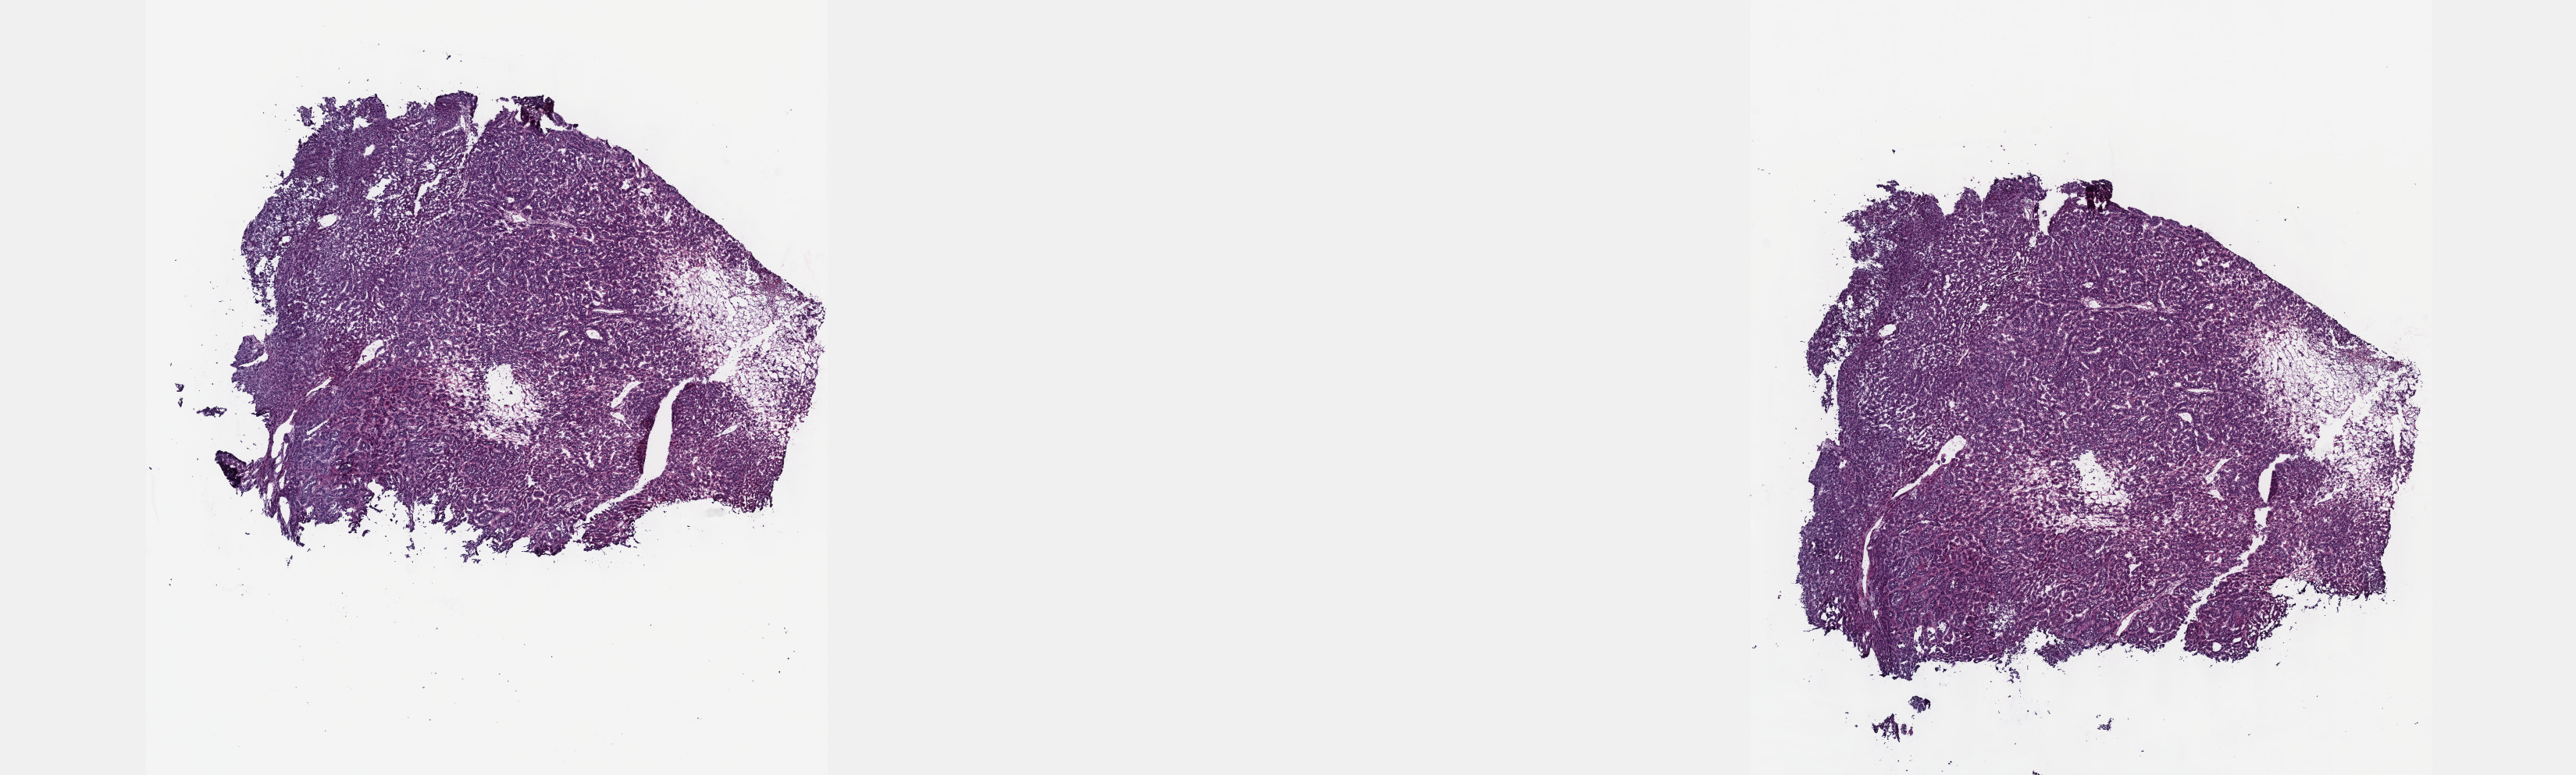
Whole-slide histology image, H&E, whole scanned area (about 26.7 x 8.0 mm, slide scanned at 40x) shown as a low-resolution overview, frozen section from the top of the tissue portion, sample: primary tumour, liver. Female, age 59 years at initial diagnosis. Histologic grade: G3 (poorly differentiated). Slide review estimates, as recorded: tumour cells 100%, tumour nuclei 80%, normal cells 0%, stromal cells 0%, necrosis 0%. Infiltration values recorded for this section: lymphocyte infiltration 2%, monocyte infiltration 0%, neutrophil infiltration 0%.
TNM: T3a N0 M0. AJCC pathologic stage: IIIA (7th edition). Pathologic diagnosis: Hepatocellular carcinoma, NOS.